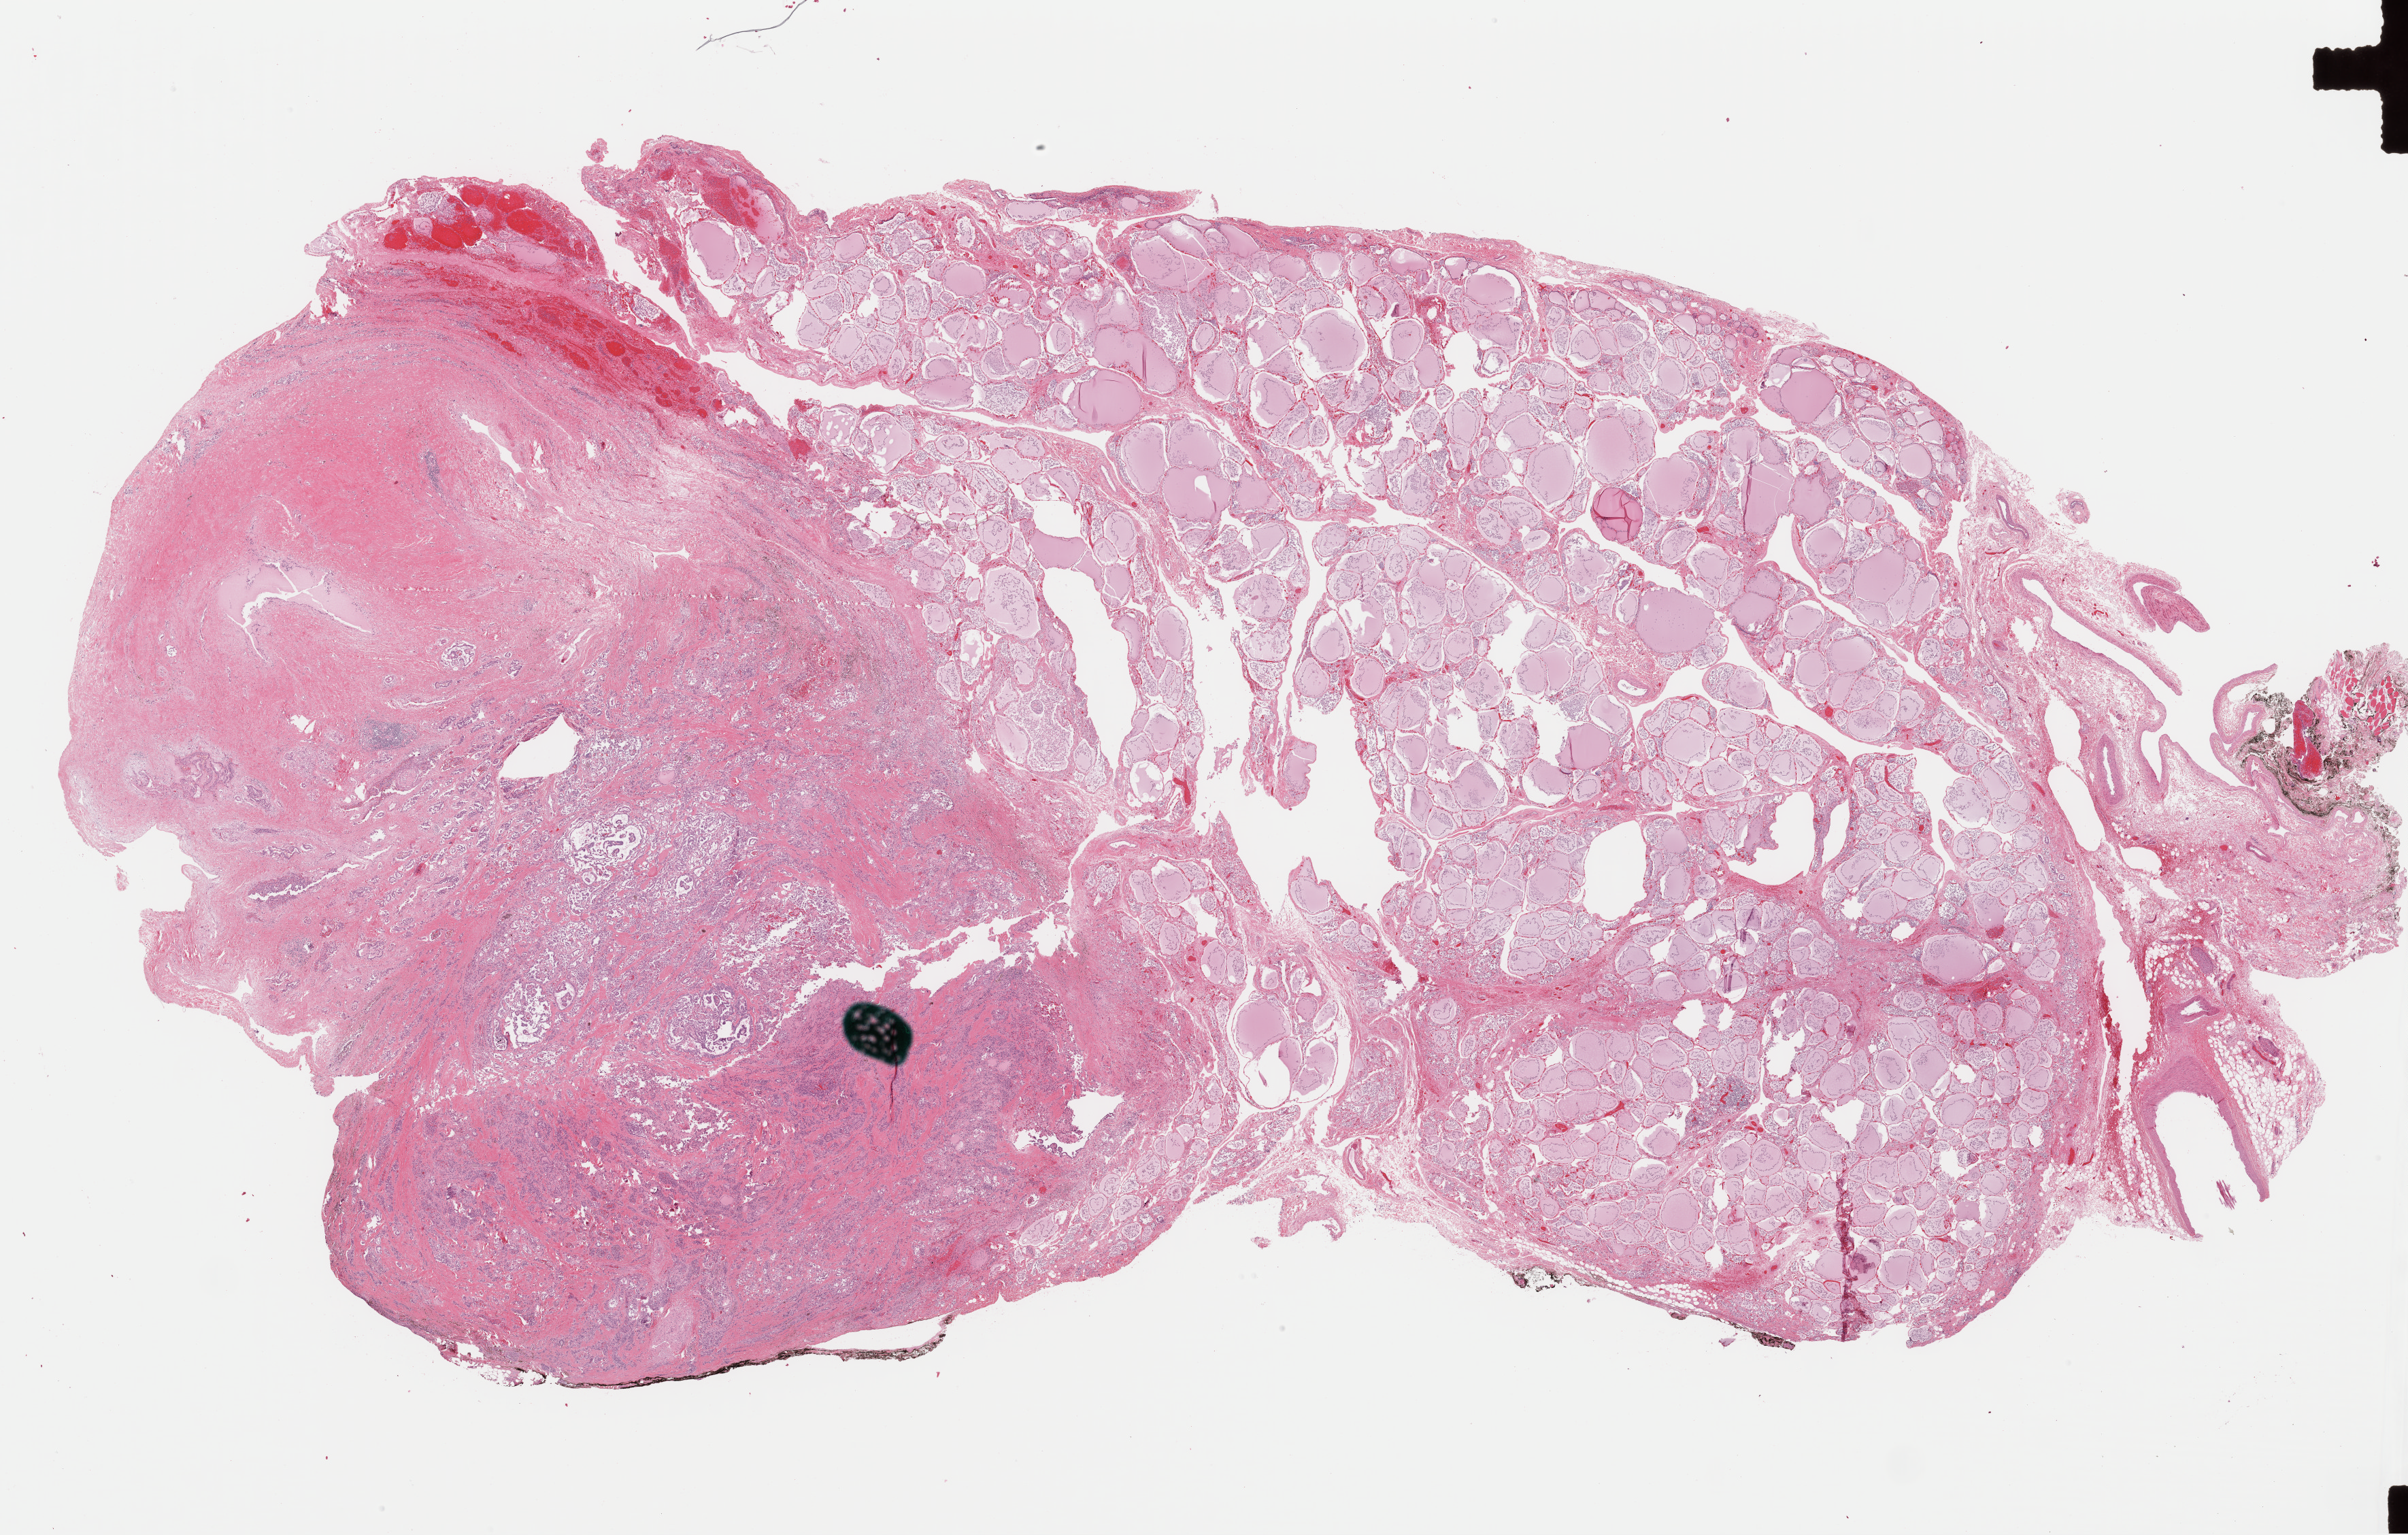
Digitized H&E tissue section (whole slide), low-resolution overview of the scanned area, about 28.0 x 17.8 mm (from a 40x scan). Formalin-fixed paraffin-embedded (FFPE) diagnostic section. Sample: primary tumour, thyroid. Male, age 45 years at initial diagnosis.
* diagnosis: Papillary adenocarcinoma, NOS (thyroid gland)
* AJCC pathologic stage: III